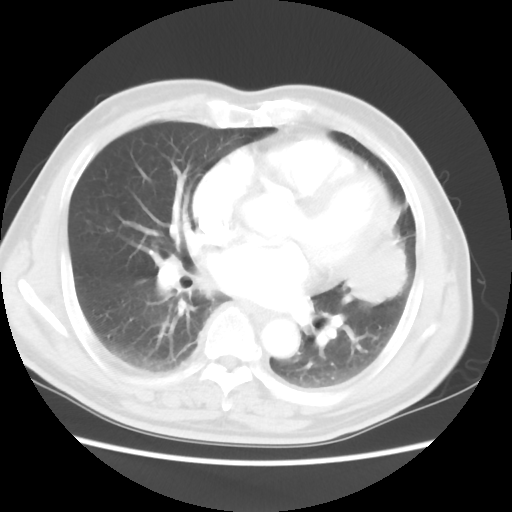
Chest CT, one axial slice. Slice 22 of 50 in the series (ordered by position). Reconstruction kernel STANDARD. 120 kVp. Lung window (W 1500 / L -600 HU). 5 mm slice thickness. 512 × 512 image matrix, field of view 360 × 360 mm. Male patient, age 69 years. From the clinical record (not read from this slice): clinical TNM (as recorded): T3 N1 M1a.
Annotated regions visible in this slice (rectangle marked by the reading radiologist):
- lung tumour (recorded histology: squamous cell carcinoma): bounding box (x1, y1, x2, y2) in pixels: (327, 203, 412, 311)